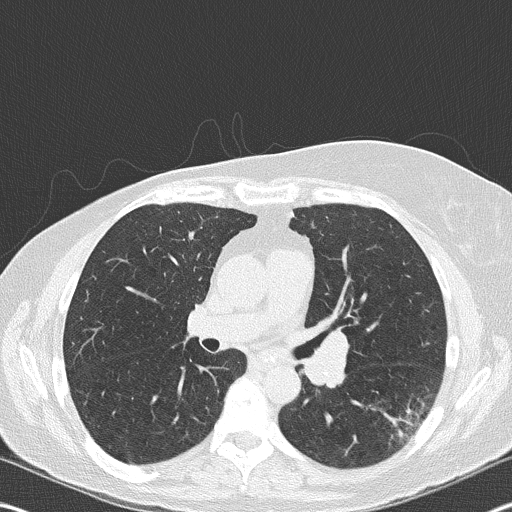
Low-dose screening chest CT, one axial slice. Slice 104 of 177 in the series (ordered by position). Reconstruction kernel B50f. Lung window (W 1500 / L -600 HU). 2 mm slice thickness. 512 × 512 image matrix, field of view 342 × 342 mm.
Annotated regions visible in this slice (outlined manually by an expert reader):
- lesion 1 (tumor): bounding box <384,409,420,438> (left, top, right, bottom; pixels)
- lesion 2 (nodule, hilum of left lung): <310,340,346,383>